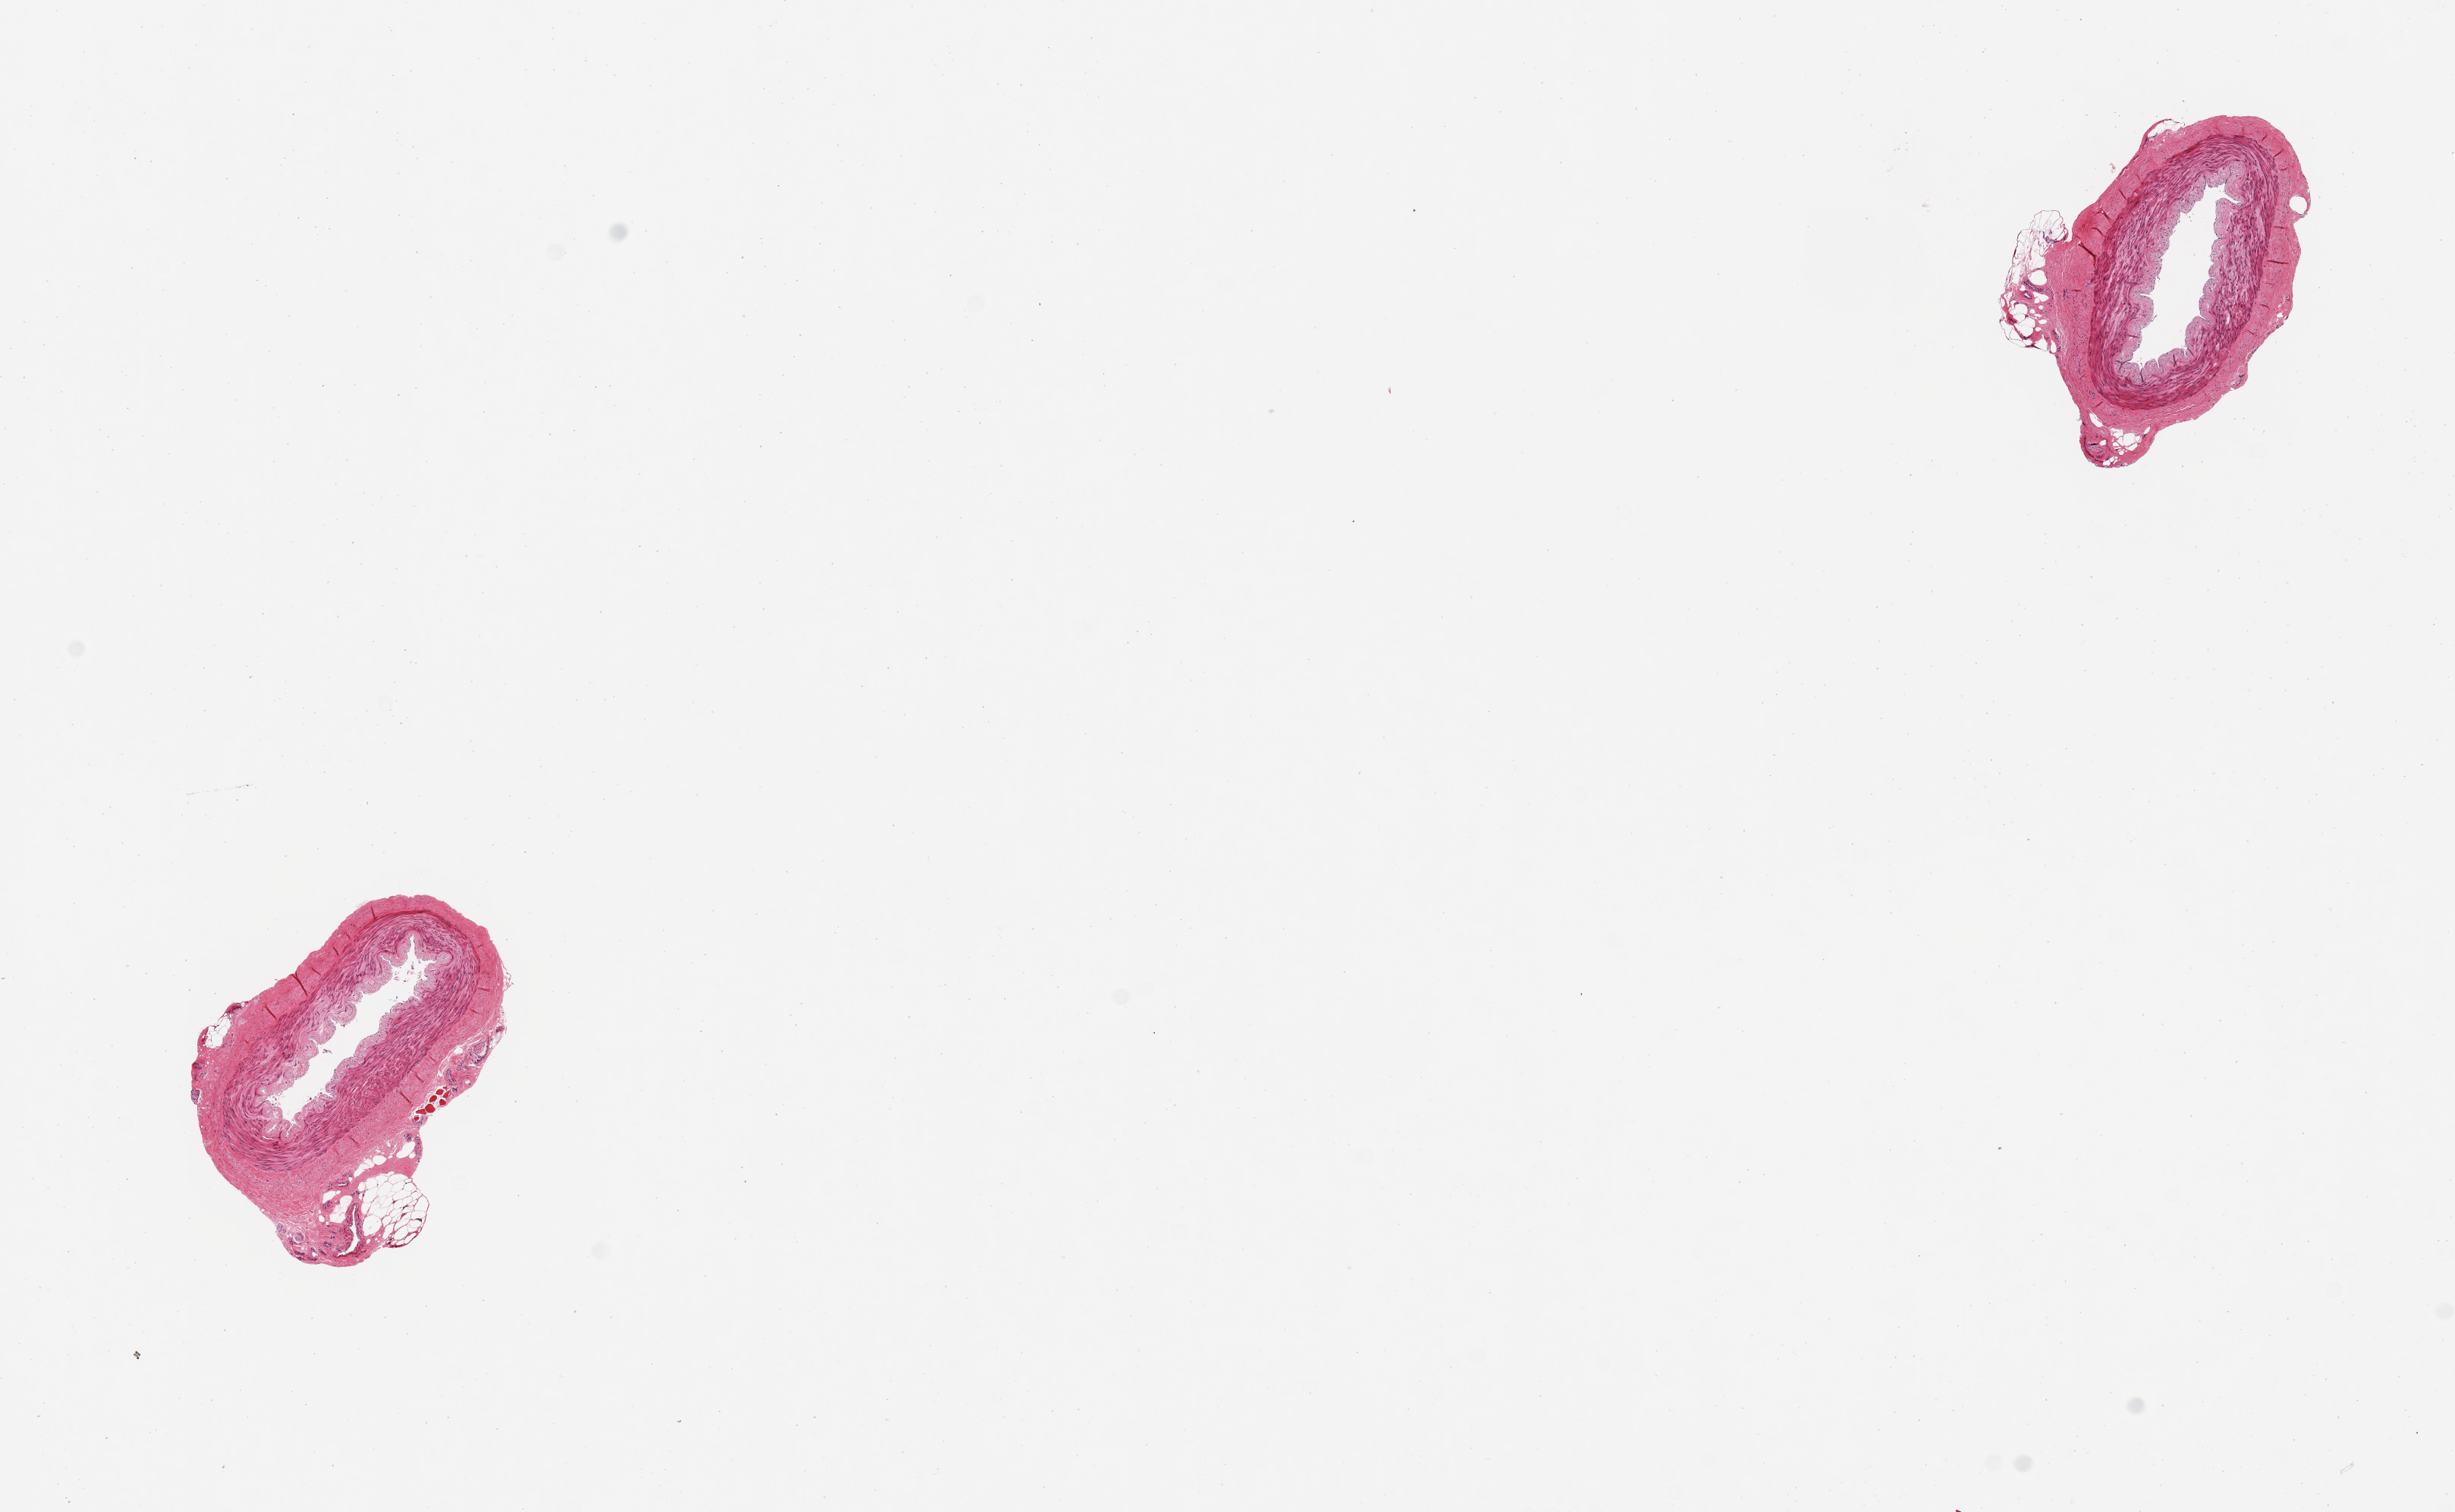
Whole-slide image, haematoxylin and eosin stain — a low-resolution overview of the entire scanned area, about 12.8 x 7.9 mm (acquisition: 20x scan); PAXgene-fixed paraffin-embedded (PFPE) section; target tissue: tibial artery; tissue donor sample. Donor sex: female.
- pathologist's review note for this sample: 2 pieces, generally clean sections, no atherosis